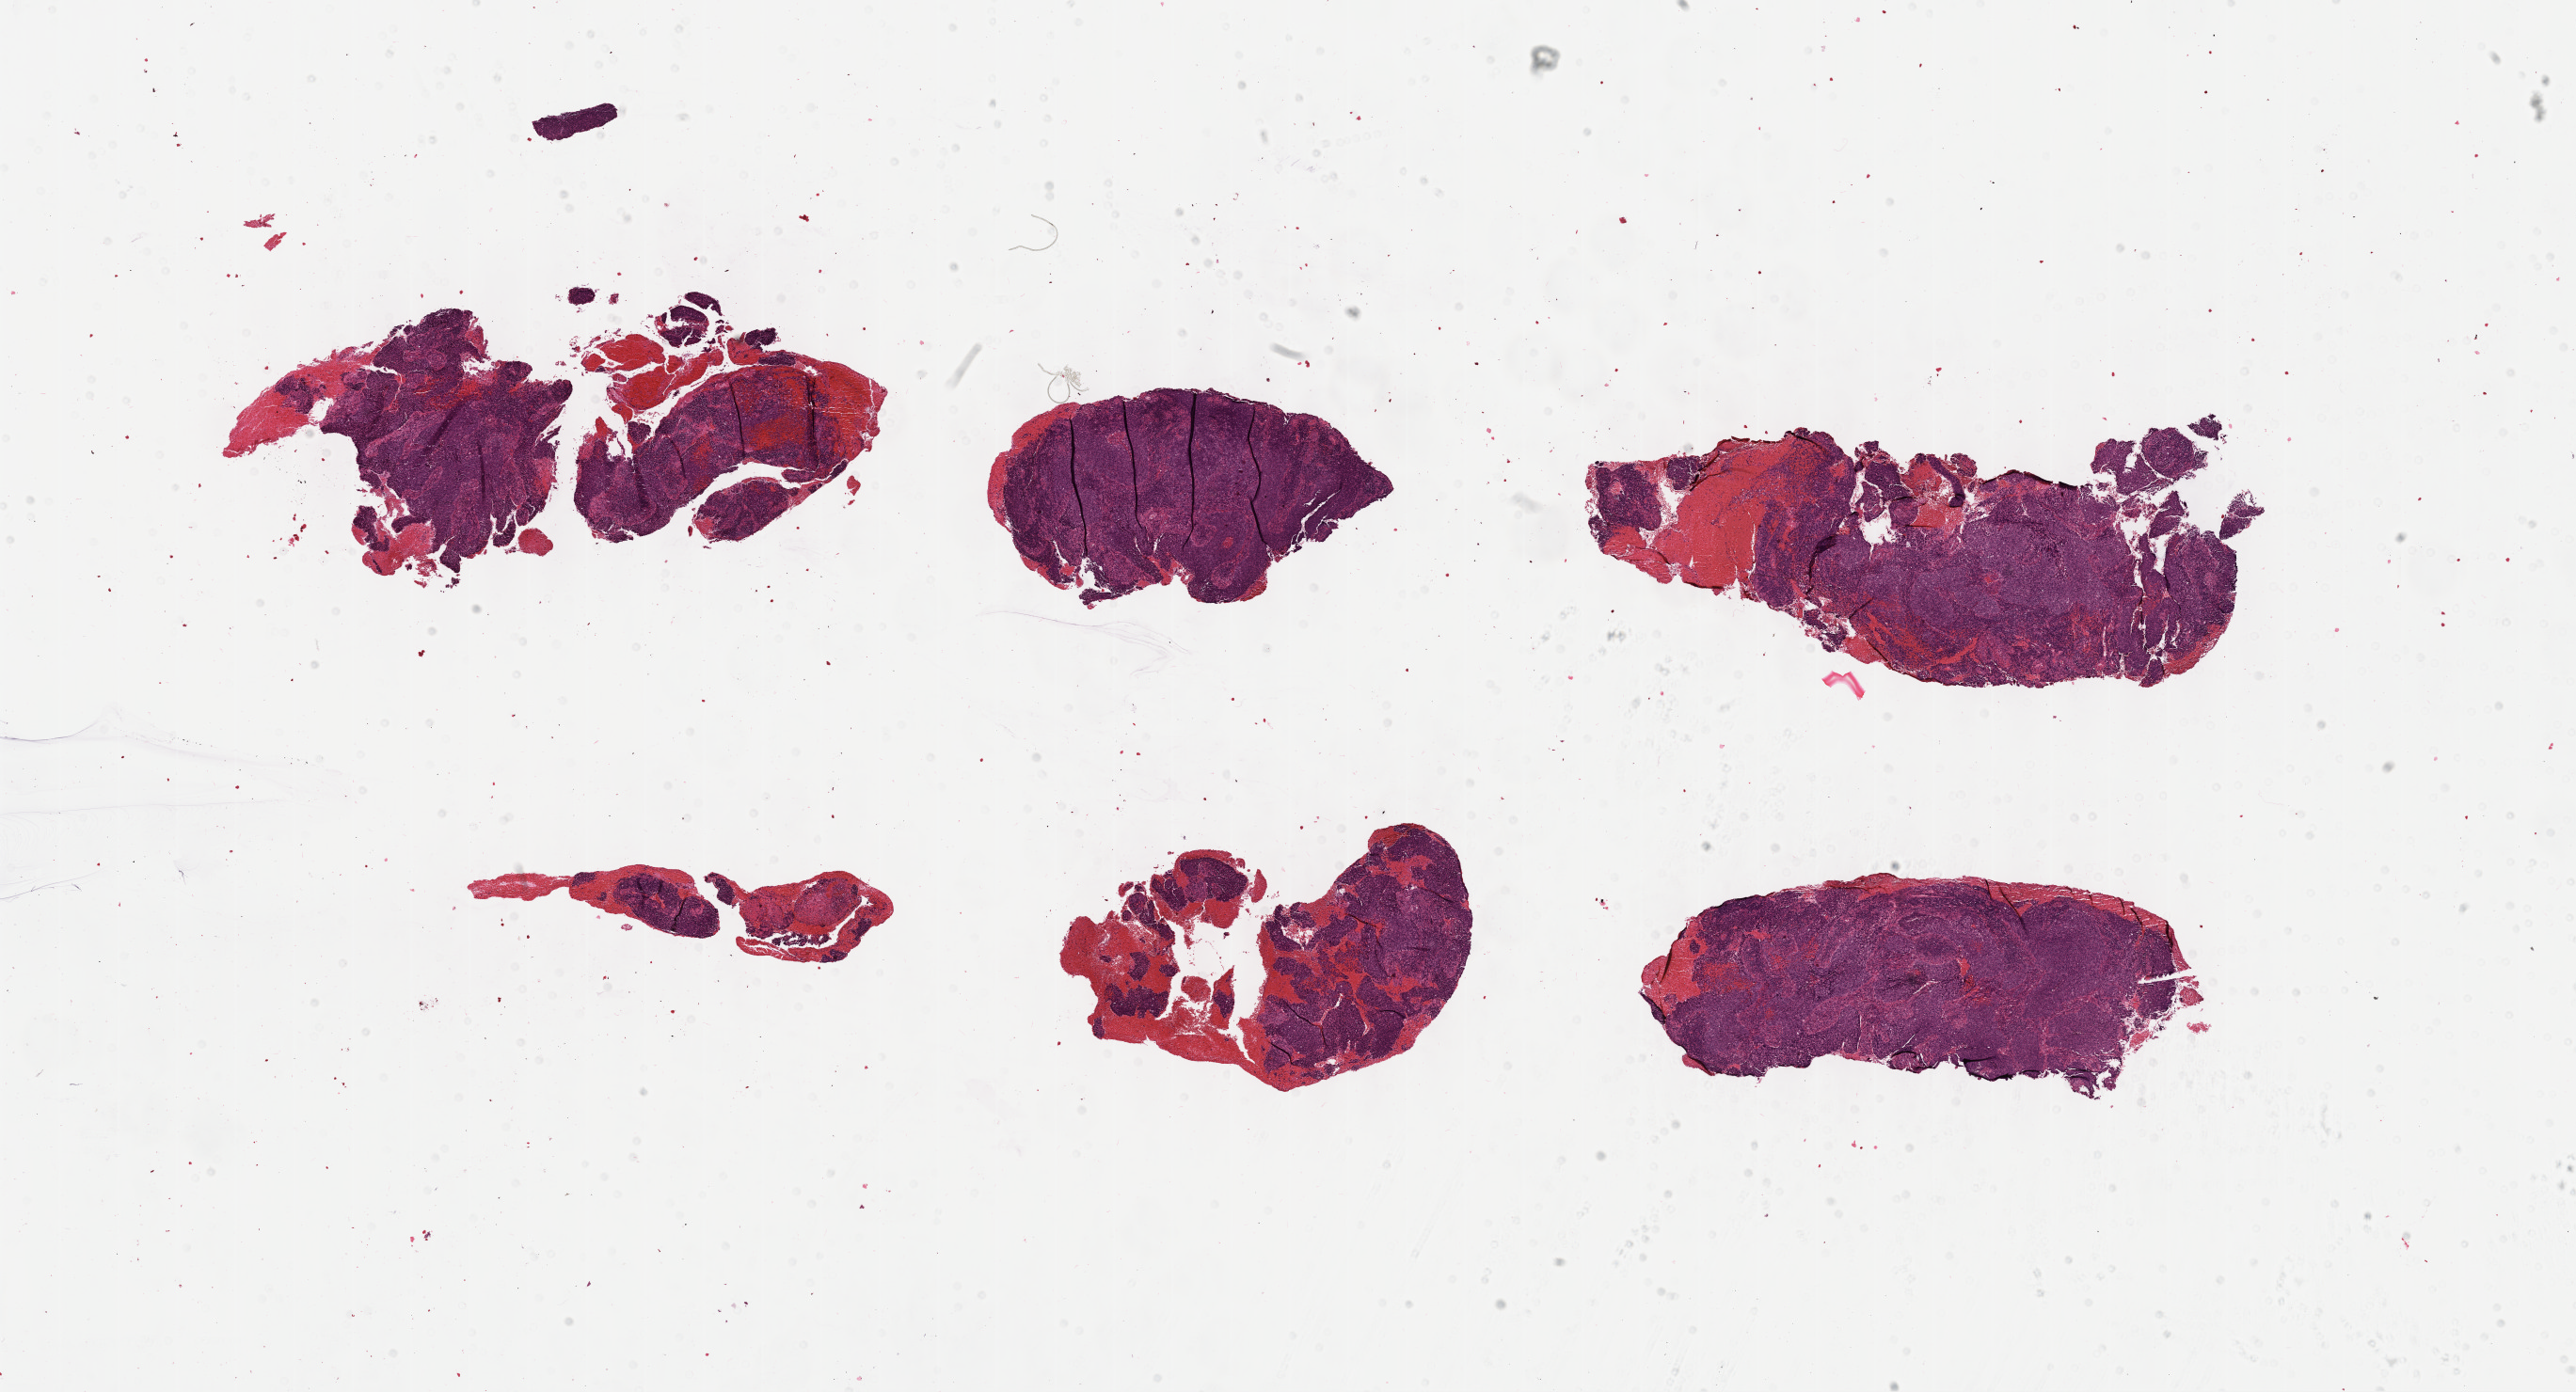
Whole-slide histology image, Hematoxylin and eosin (H&E) stained, a low-resolution overview of the entire scanned area, about 22.1 x 12.0 mm (from a 40x scan). Formalin-fixed paraffin-embedded (FFPE) diagnostic section. Primary tumour sample from the cervix. Female patient; age at initial diagnosis 73 years.
* pathologic diagnosis: Squamous cell carcinoma, large cell, nonkeratinizing, NOS (cervix uteri)